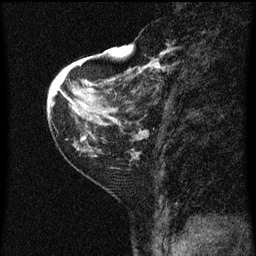
Breast MRI (dynamic contrast-enhanced), one sagittal slice. Position 19 of 60 along the scan axis. Dynamic contrast-enhanced series, image 2 of 3 at this slice position (ordered by acquisition). 1.5 T. TE 4.2 ms, TR 8 ms. 2 mm slice thickness. 256 × 256 image matrix. Patient: female, 48 years.
Outlined on this slice (semi-automatically segmented with operator editing):
- analysis volume of interest (the breast-tissue region the enhancement analysis was run in; not a lesion): bounding box [x1, y1, x2, y2] px = [128, 54, 175, 125]
- tumour enhancement mask (voxels above the 70 % enhancement threshold inside the analysis volume of interest): [135, 54, 166, 91]